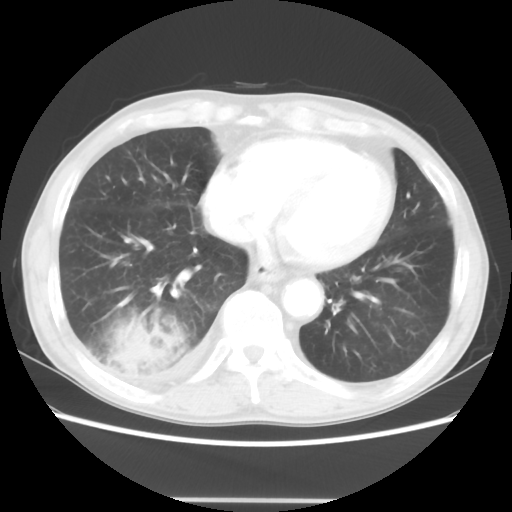
Chest CT, one axial slice. Position 12 of 48 along the scan axis. Reconstruction kernel STANDARD. Lung window (W 1500 / L -600 HU). 5 mm slice thickness. 512 × 512 image matrix. Male patient, age 66 years. From the clinical record (not read from this slice): clinical TNM (as recorded): T4 N1 M1.
Annotated regions visible in this slice (bounding box drawn by a radiologist):
- lung tumour (recorded histology: small cell carcinoma): bounding box <100,308,188,390> (left, top, right, bottom; pixels)